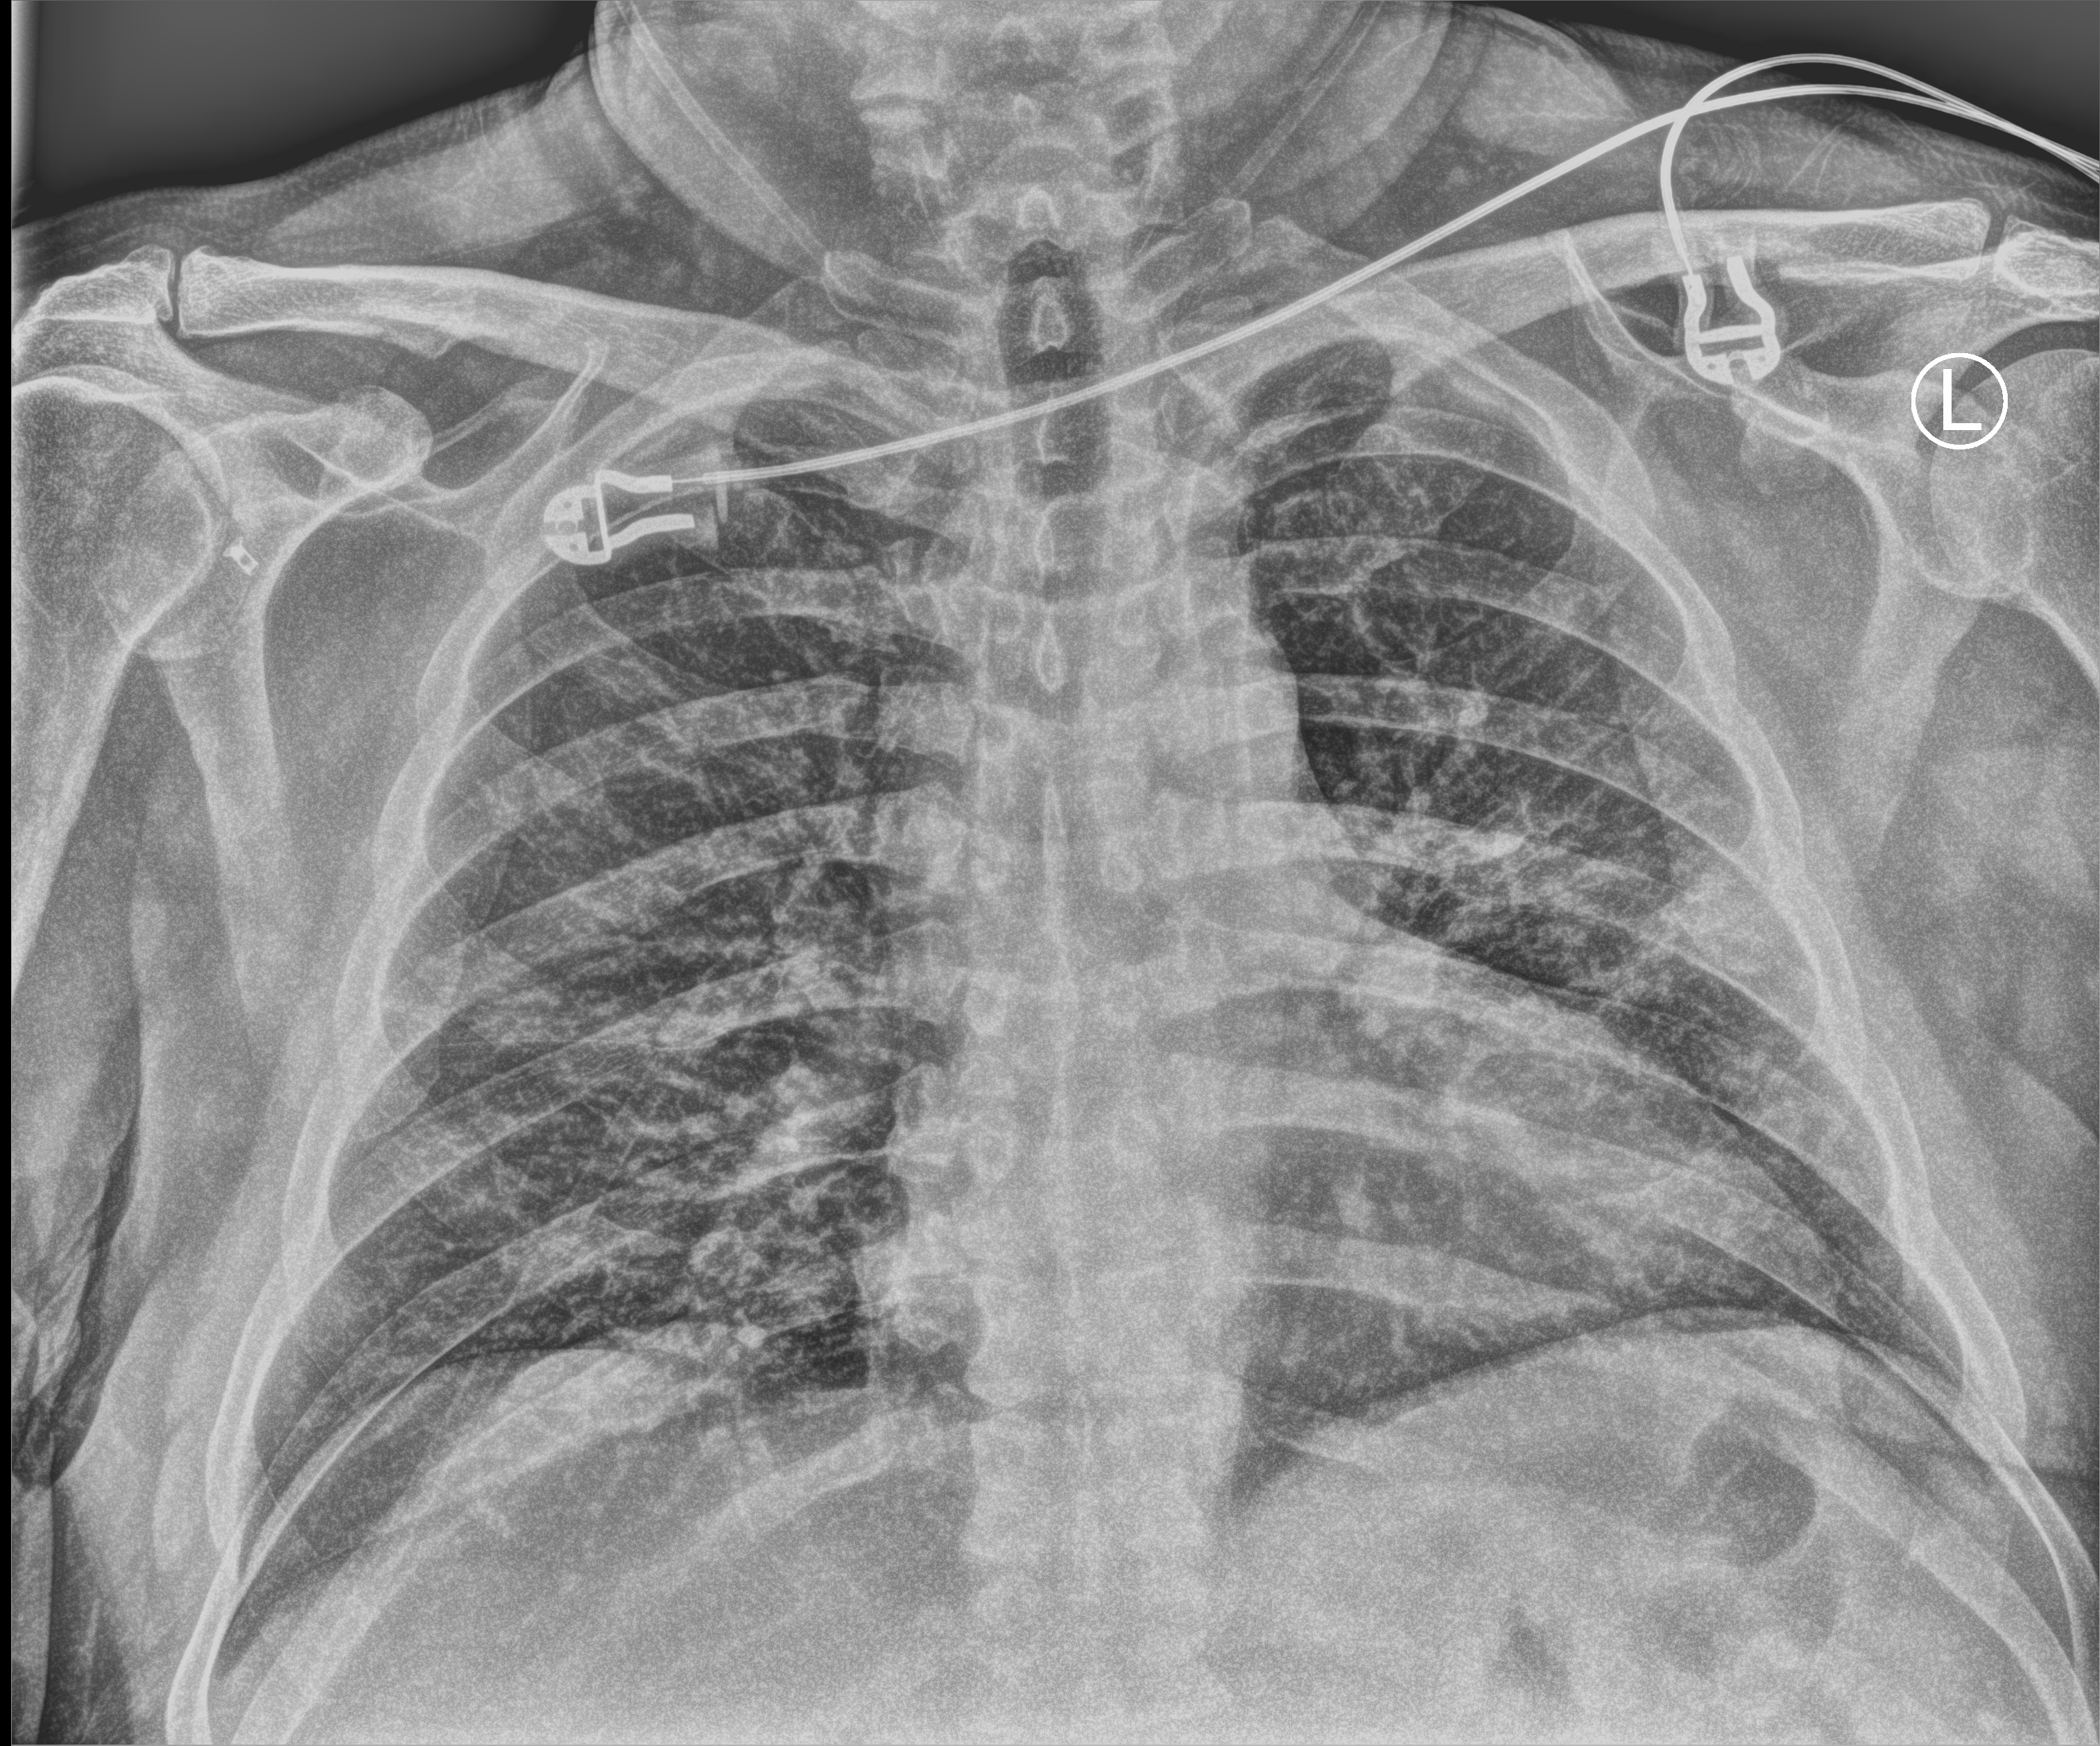
Portable chest radiograph, anteroposterior (AP) projection. Male patient hospitalised with COVID-19, age 18–59 years.
Admission-level facts for this patient (not findings on this image; timing relative to this image not recorded): mechanically ventilated during this hospital stay: yes; COPD (admission record): no.